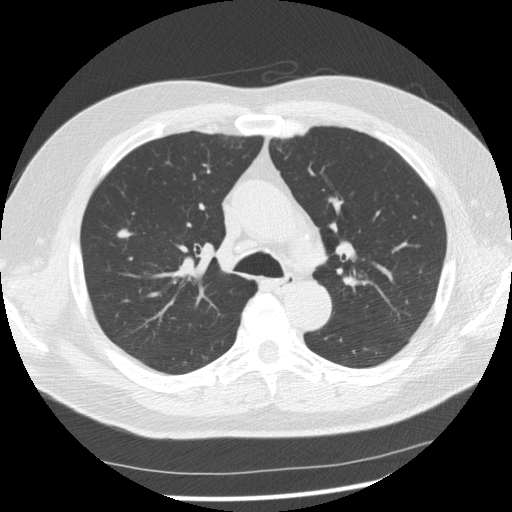
Chest CT (low-dose screening protocol), one axial image; second screening round (one year after baseline); lung window (W 1500 / L -600 HU); standard (soft-tissue) reconstruction kernel (STANDARD). Male, age 61 years at enrolment. Current smoker at enrolment.
• Expert-annotated lung lesion, bounding box <100,221,139,254> (left, top, right, bottom; pixels).
• The exam's reader record, not a measurement of the box and not confirmed to be the same lesion: non-calcified nodule or mass ≥4 mm, right upper lobe, 7 × 7 mm, smooth margins, soft tissue attenuation, pre-existing on the prior screen: yes; interval growth: no.
• Official screen result: positive, no significant change: stable abnormalities potentially related to lung cancer, unchanged since the prior screening exam.
• Lung cancer was diagnosed 389 days after this screen: adenocarcinoma, NOS, right upper lobe, stage IIIA (AJCC 6th edition), 13 mm at pathology.